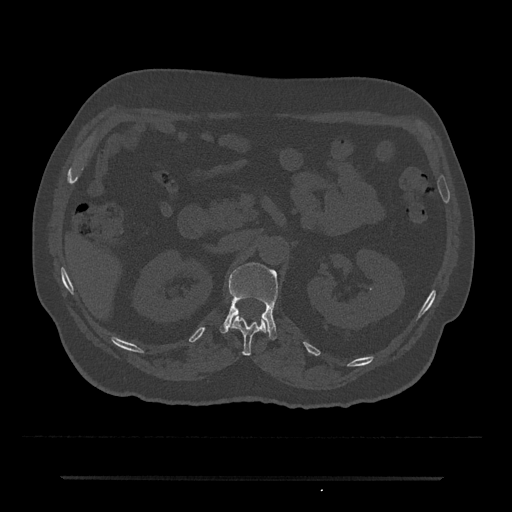
CT including the spine, one axial slice; position 96 of 797 along the scan axis; 120 kVp; bone window (W 1800 / L 400 HU); 512 × 512 image matrix, field of view 437 × 437 mm. Patient: male, 69 years. From the clinical record (not read from this slice): primary cancer: prostate.
Structures marked on this image (semi-automatically segmented with operator editing):
- L1 vertebra: bounding box [x1, y1, x2, y2] px = [220, 262, 278, 340]
- T12 vertebra: [231, 314, 268, 355]